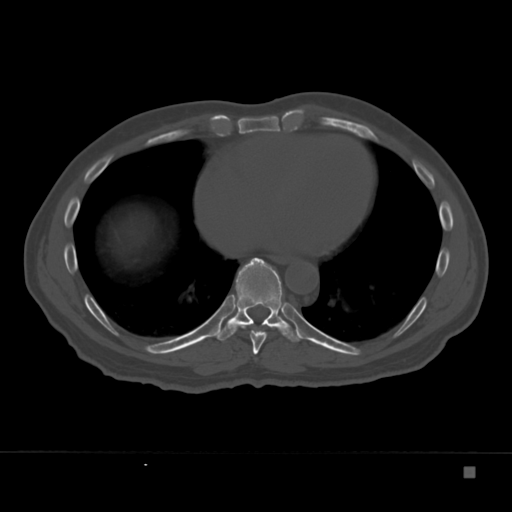
CT including the spine, one axial slice. Slice 197 of 332 in the series (ordered by position). Reconstruction kernel Br40s. 120 kVp. Bone window (W 1800 / L 400 HU). 512 × 512 image matrix, field of view 389 × 389 mm. Patient: male, 72 years. From the clinical record (not read from this slice): primary cancer: skeletal.
Annotated regions visible in this slice (semi-automatically segmented with operator editing):
- T8 vertebra: bounding box [x1, y1, x2, y2] px = [242, 326, 272, 355]
- T9 vertebra: [213, 258, 303, 342]